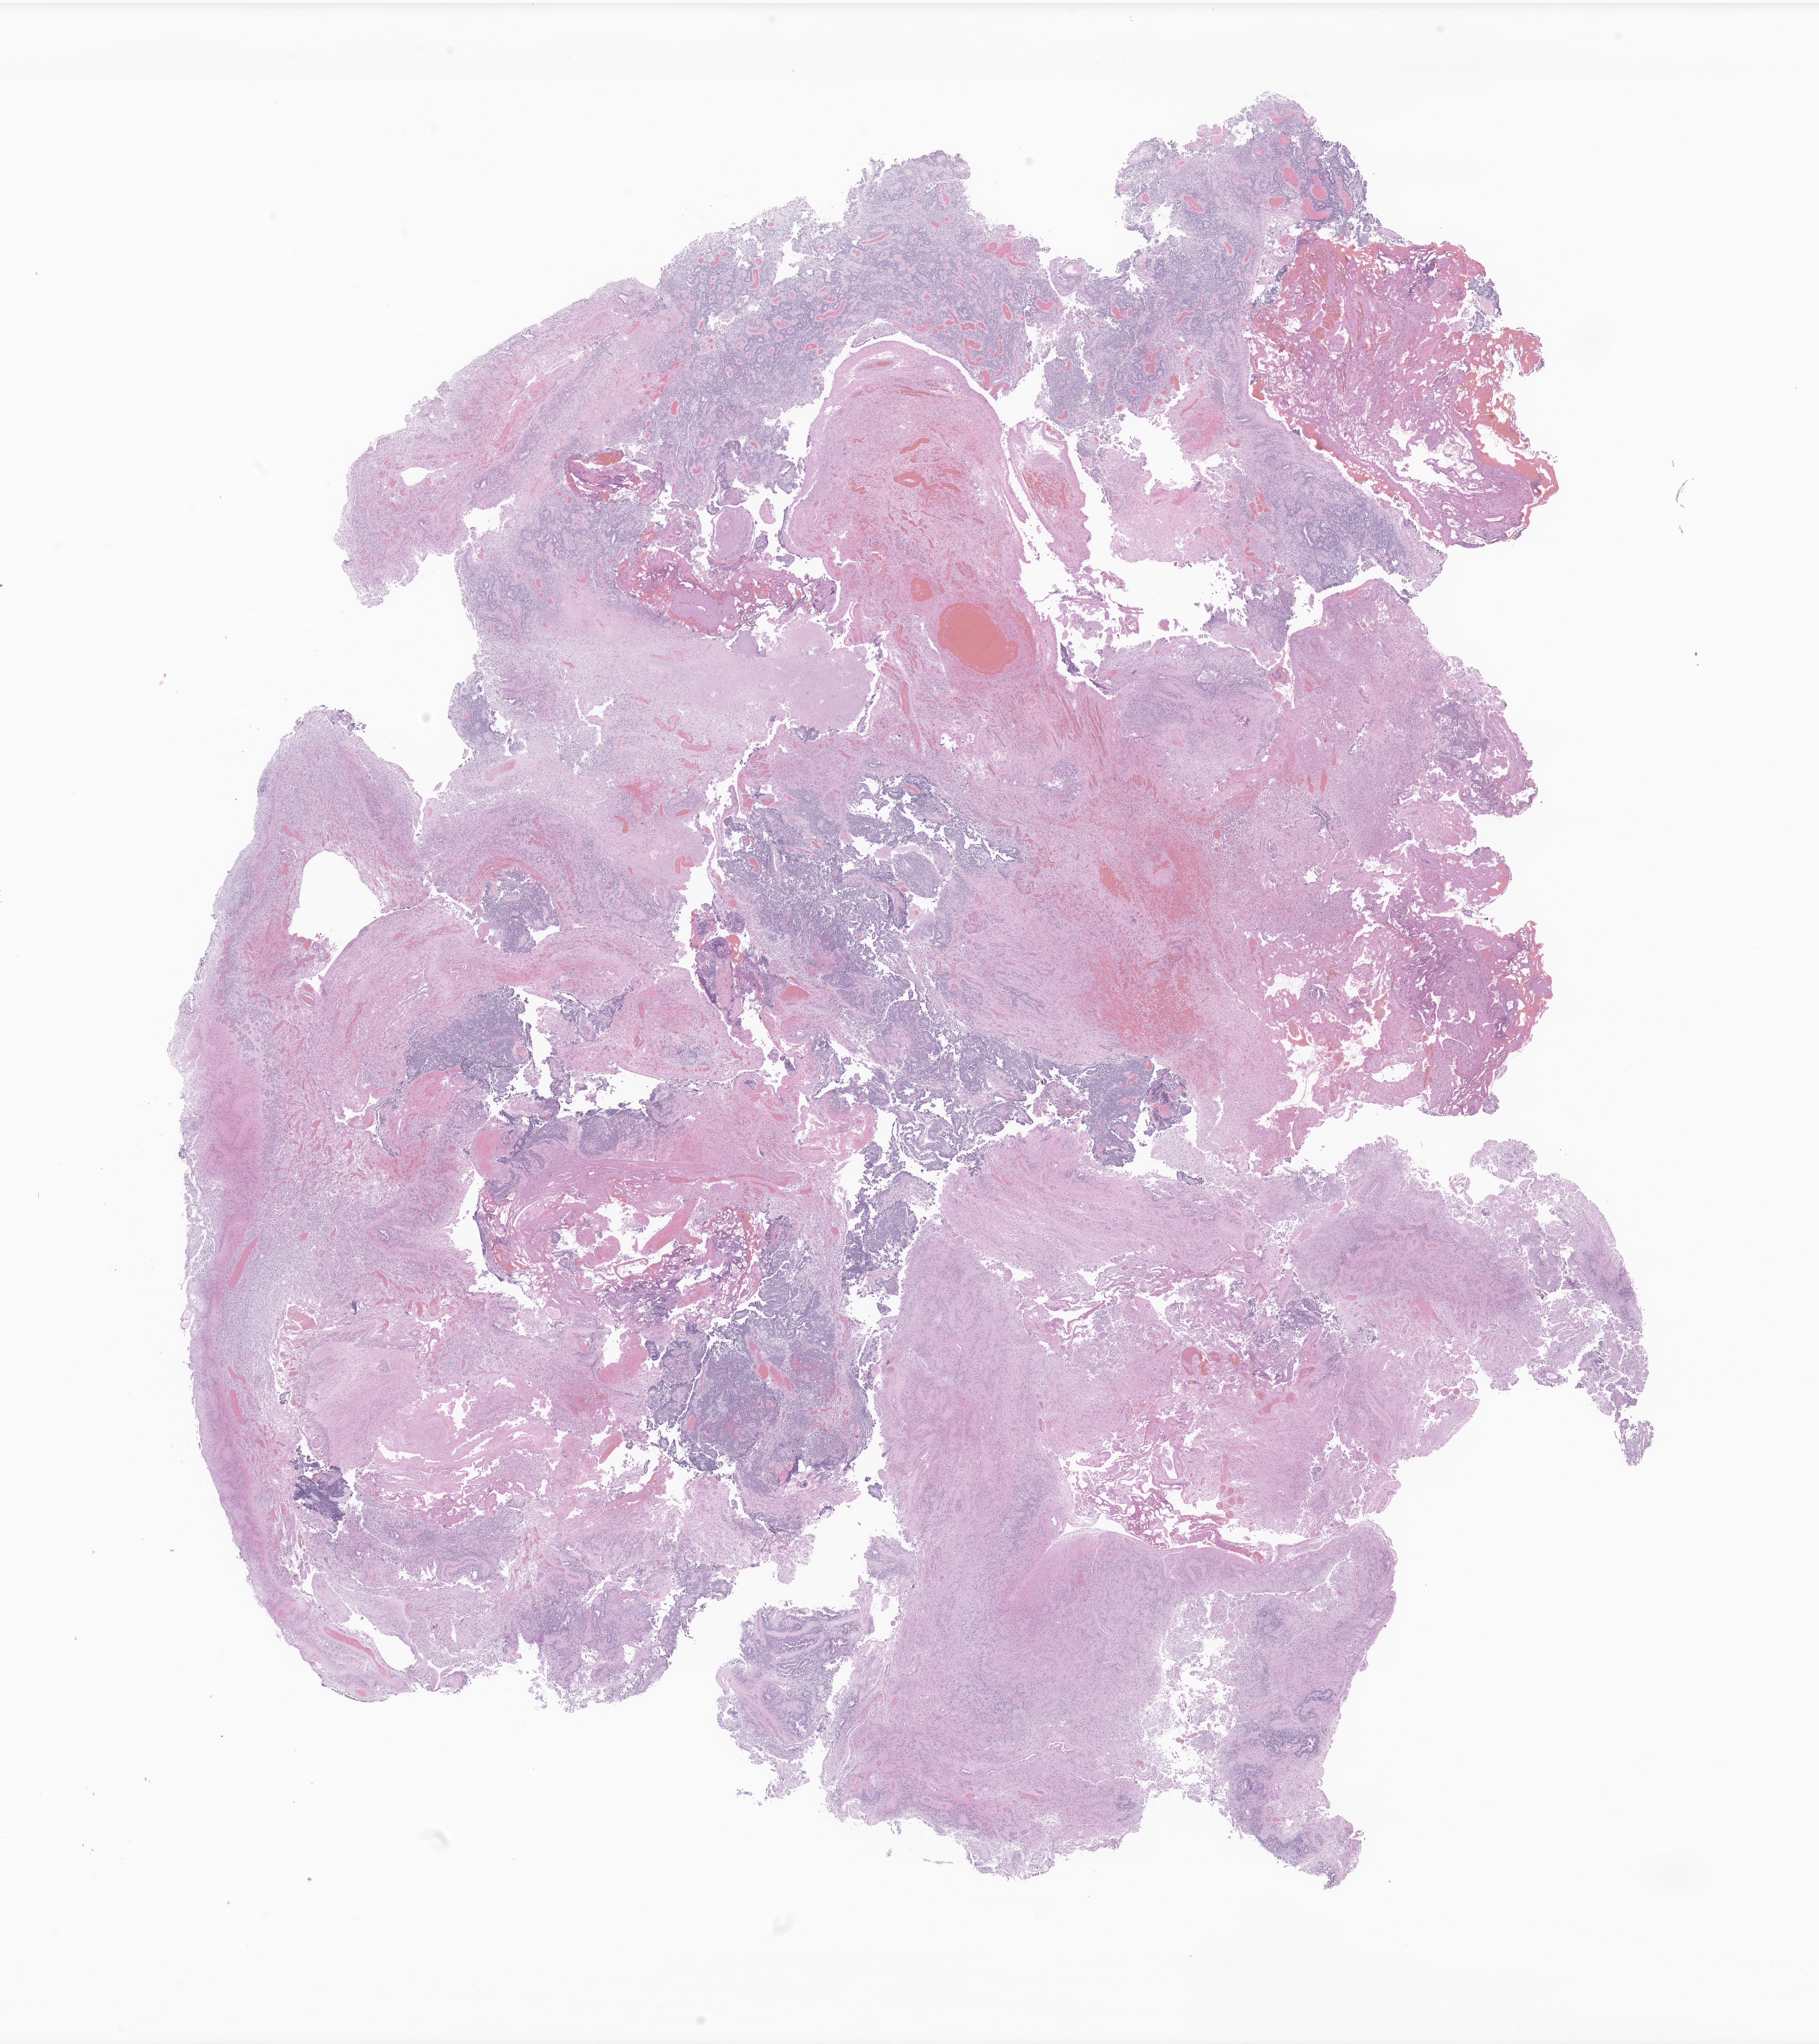
Whole-slide image, H&E stain of tumor tissue from the brain — low-resolution overview of the scanned area, about 20.7 x 23.2 mm. Formalin-fixed paraffin-embedded section. Female patient, age 840 days (about 2.3 years).
* recorded diagnosis: Ependymoma, NOS